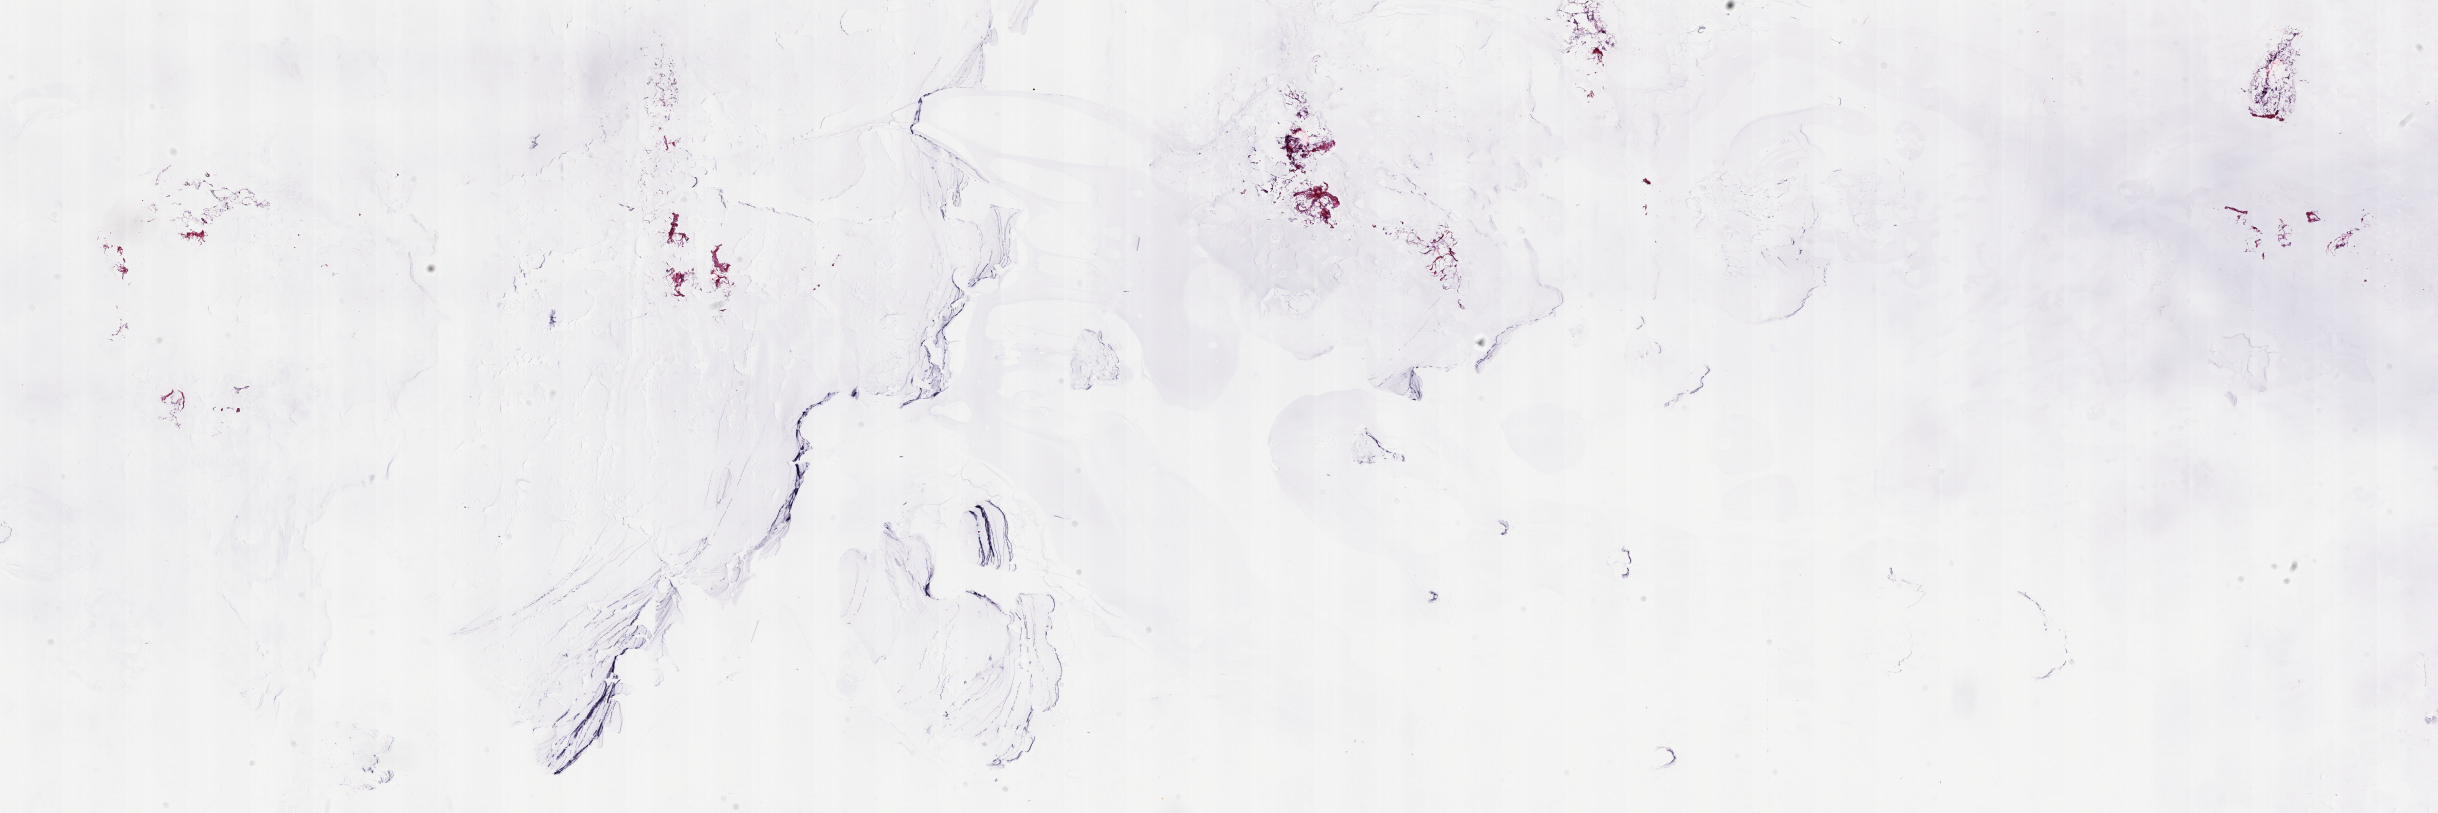
Hematoxylin and eosin (H&E) stained whole-slide image, low-resolution overview of the scanned area, about 38.7 x 12.9 mm; frozen section from the top of the tissue portion; breast, solid tissue normal (non-tumour tissue) sample. Patient: female, age at initial diagnosis 84 years. Pathologist review of this section (percent, as recorded): tumour cells 0%, tumour nuclei 0%, normal cells 100%, stromal cells 0%, necrosis 0%. Inflammatory infiltration, as recorded: lymphocyte infiltration 1%, monocyte infiltration 0%, neutrophil infiltration 0%.
This section: solid tissue normal sample (biorepository sample class). Patient diagnosis: Infiltrating duct carcinoma, NOS.